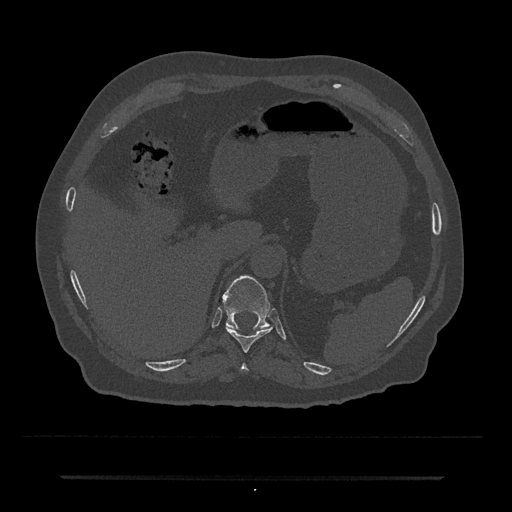
CT including the spine, one axial slice. Slice 209 of 797 in the series (ordered by position). Reconstruction kernel Br40s/3. Bone window (W 1800 / L 400 HU). 0.5 mm slice thickness. 512 × 512 image matrix. Patient: male, 69 years. Case-level facts recorded for this patient, not image findings: primary cancer: prostate.
Structures marked on this image (semi-automatic segmentation, software-assisted and operator-edited):
- T10 vertebra: box from (x=226, y=326) to (x=272, y=352) px
- T11 vertebra: (x=222, y=275)–(x=270, y=330)
- T9 vertebra: (x=241, y=363)–(x=248, y=371)